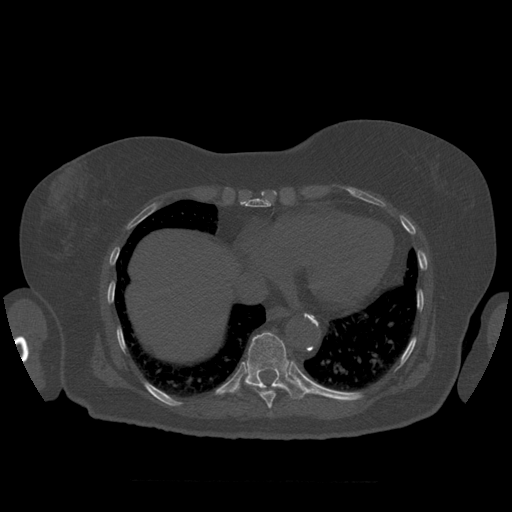
CT including the spine, one axial slice. Reconstruction kernel STANDARD. 120 kVp. Bone window (W 1800 / L 400 HU). 512 × 512 image matrix, field of view 404 × 404 mm. Patient age 81 years. From the clinical record (not read from this slice): primary cancer: renal; vertebrae with lytic lesions (as recorded): L1.
Structures marked on this image (semi-automatic segmentation, software-assisted and operator-edited):
- T10 vertebra: bounding box [x1, y1, x2, y2] px = [232, 332, 309, 399]
- T9 vertebra: [251, 386, 276, 409]